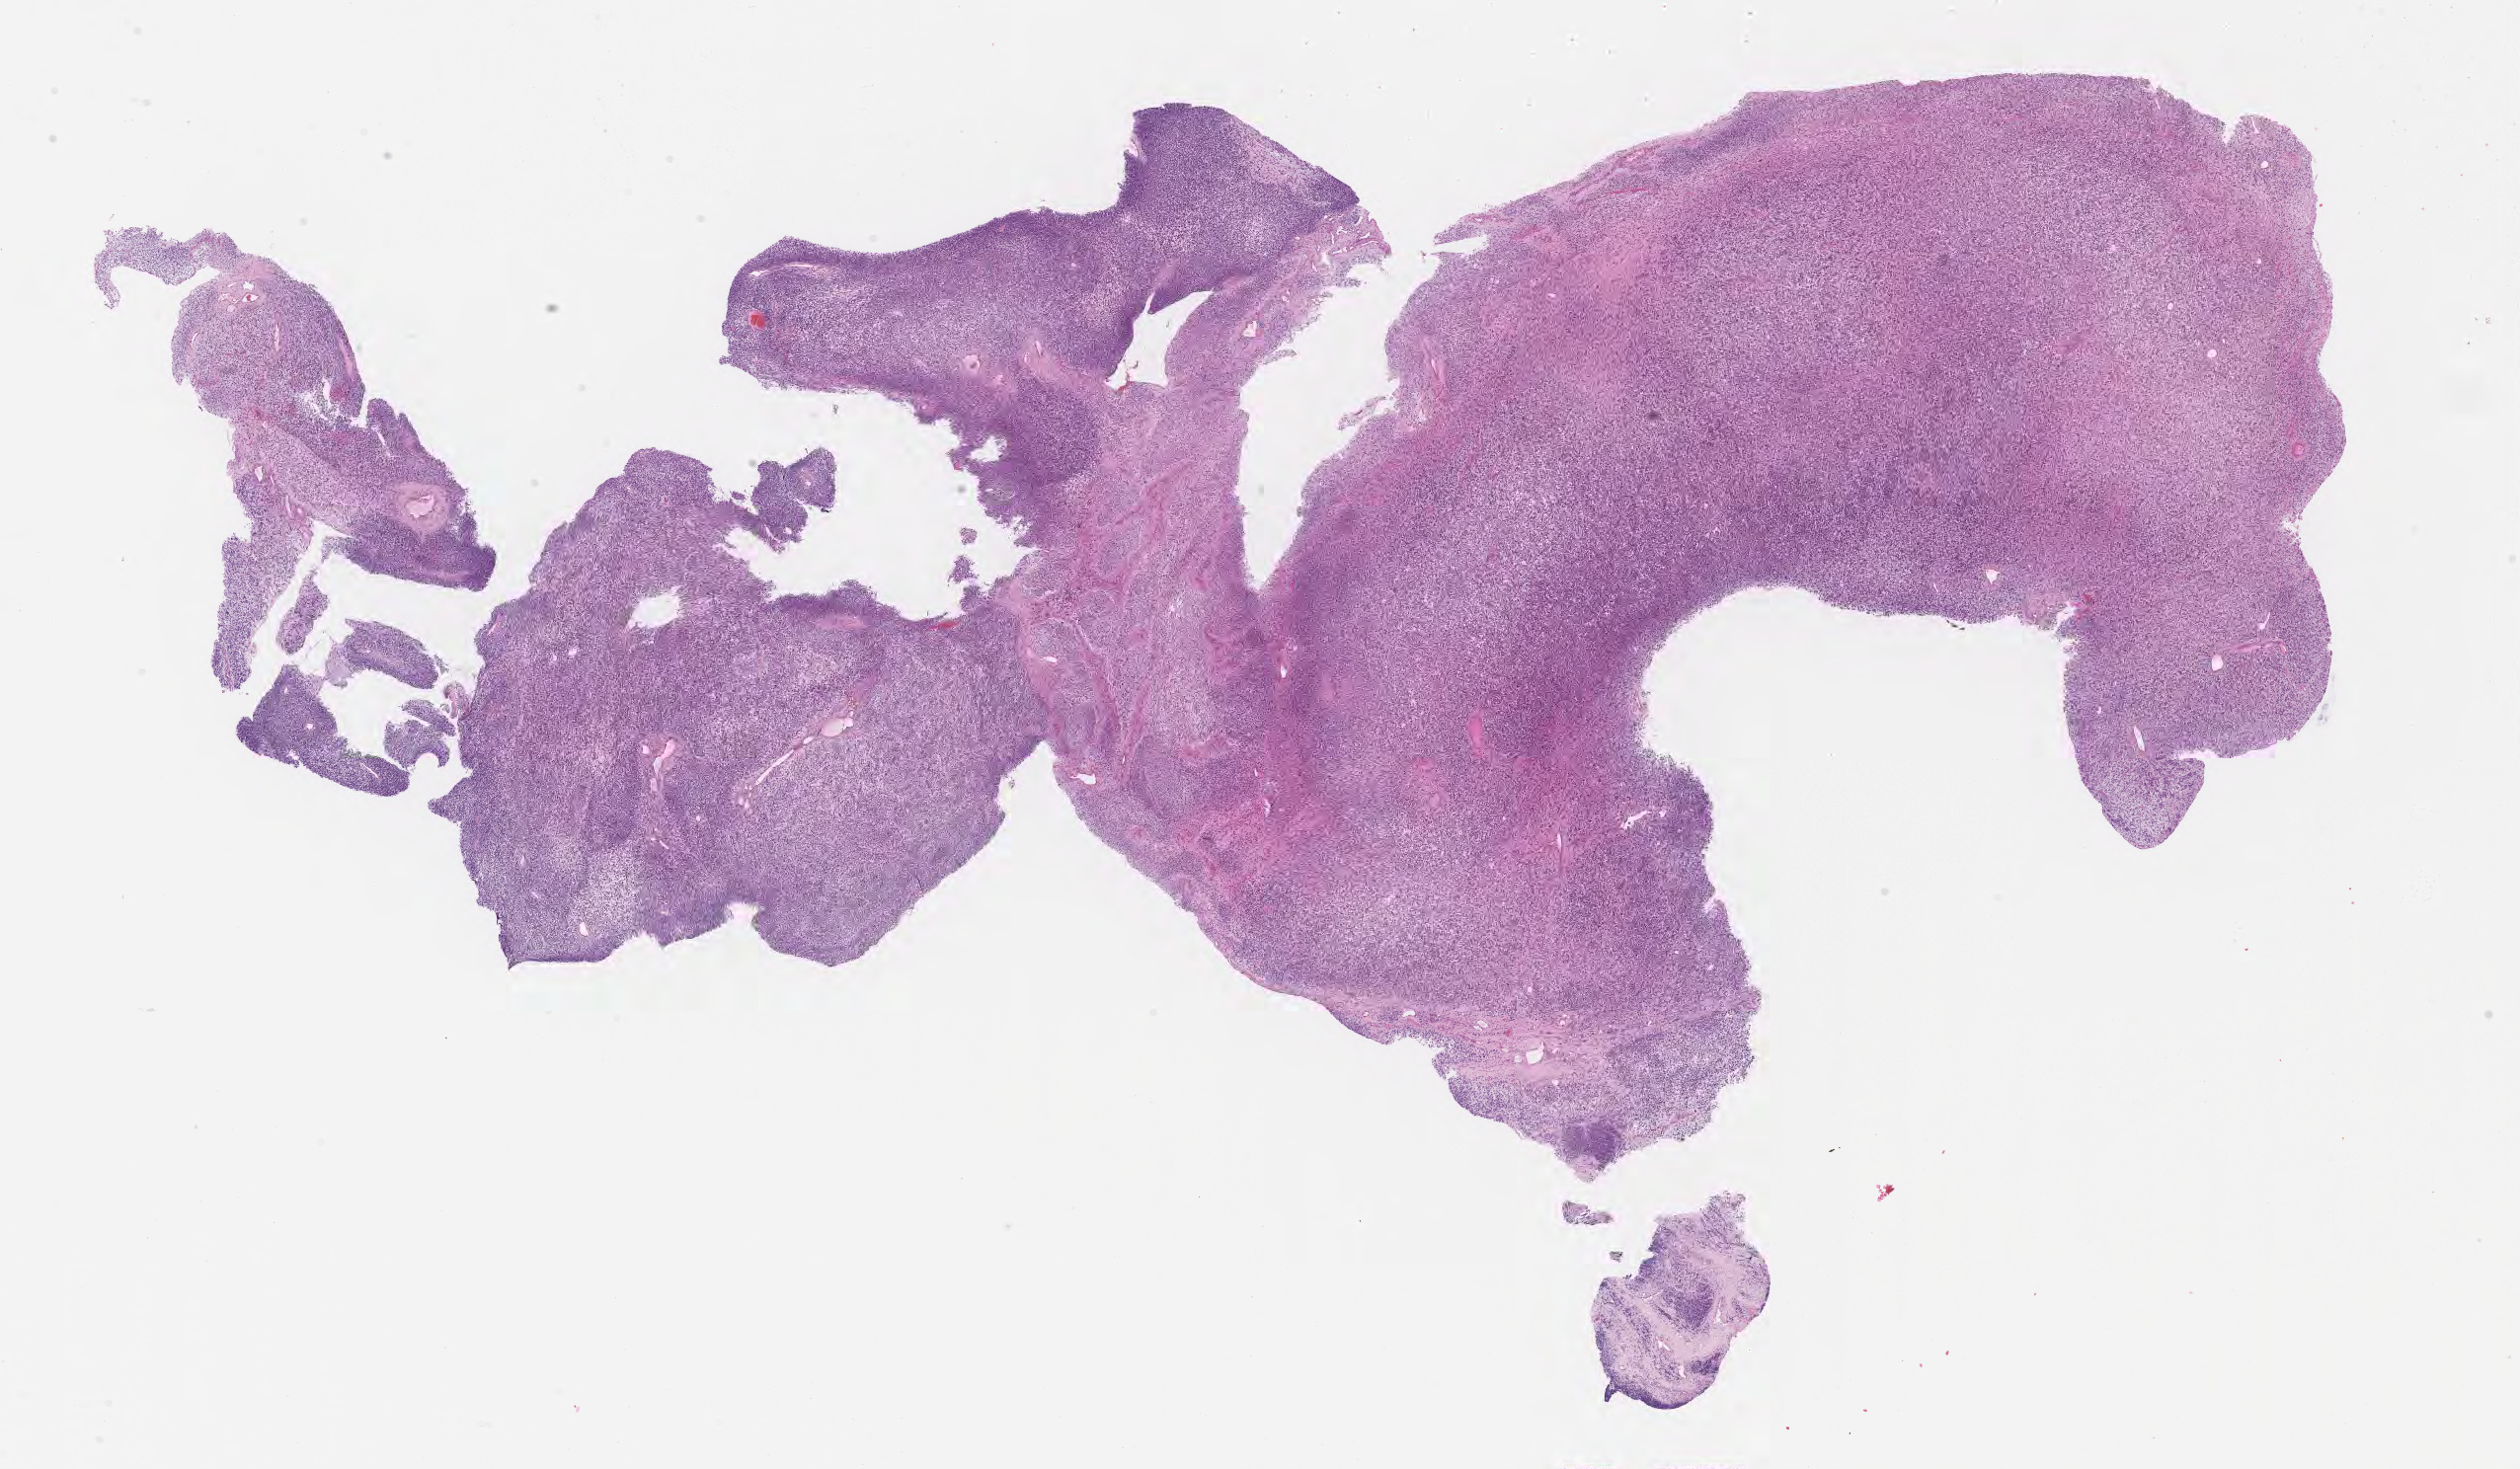
Haematoxylin and eosin whole-slide image of tumor tissue — a low-resolution overview of the entire scanned area, about 20.6 x 12.0 mm. Formalin-fixed paraffin-embedded section. Sample anatomic site: soft tissue, pelvis-left. Male patient, age at diagnosis 4.3 years.
- metastatic status at presentation (as recorded): non-metastatic (unconfirmed)
- diagnosis: rhabdomyosarcoma; histological classification: embryonal rhabdomyosarcoma
- stage (as recorded): 3